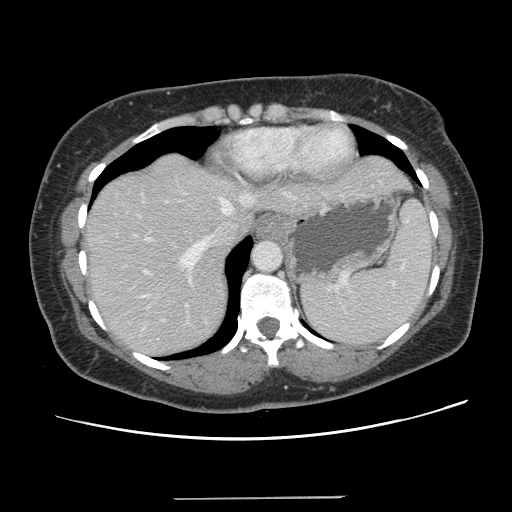
Contrast-enhanced abdominal CT, one axial slice; slice 109 of 141 in the series (ordered by position); 120 kVp; soft-tissue window (W 400 / L 40 HU); 512 × 512 image matrix, field of view 366 × 366 mm. Female patient, age 53 years. Case-level facts recorded for this patient, not image findings: diagnosis: colorectal cancer liver metastases, imaged before liver resection; multiple liver metastases: no; largest metastasis: 14.5 cm; chemotherapy before resection: yes.
Structures marked on this image (expert manual segmentation):
- hepatic veins: bounding box (x1, y1, x2, y2) in pixels: (113, 192, 296, 277)
- liver: (86, 154, 410, 357)
- planned liver remnant (the part of the liver to remain after resection): (85, 208, 255, 357)
- portal vein (with intrahepatic branches): (138, 200, 189, 324)